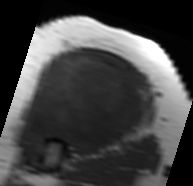
MRI of an extremity soft-tissue mass, one axial slice. Position 46 of 91 along the scan axis. MR volume resampled by the dataset authors to the PET/CT grid (not the native acquisition matrix). 193 × 186 image matrix, field of view 188 × 182 mm. Female patient. From the clinical record (not read from this slice): histological type: malignant solitary fibrous tumor; grade: intermediate; site of the primary tumour: right thigh.
Outlined on this slice (expert contour drawn on MRI and transferred to this co-registered scan by the dataset authors):
- gross tumour volume including surrounding oedema: box from (x=21, y=51) to (x=150, y=150) px
- gross tumour volume (mass): (x=26, y=51)–(x=148, y=148)